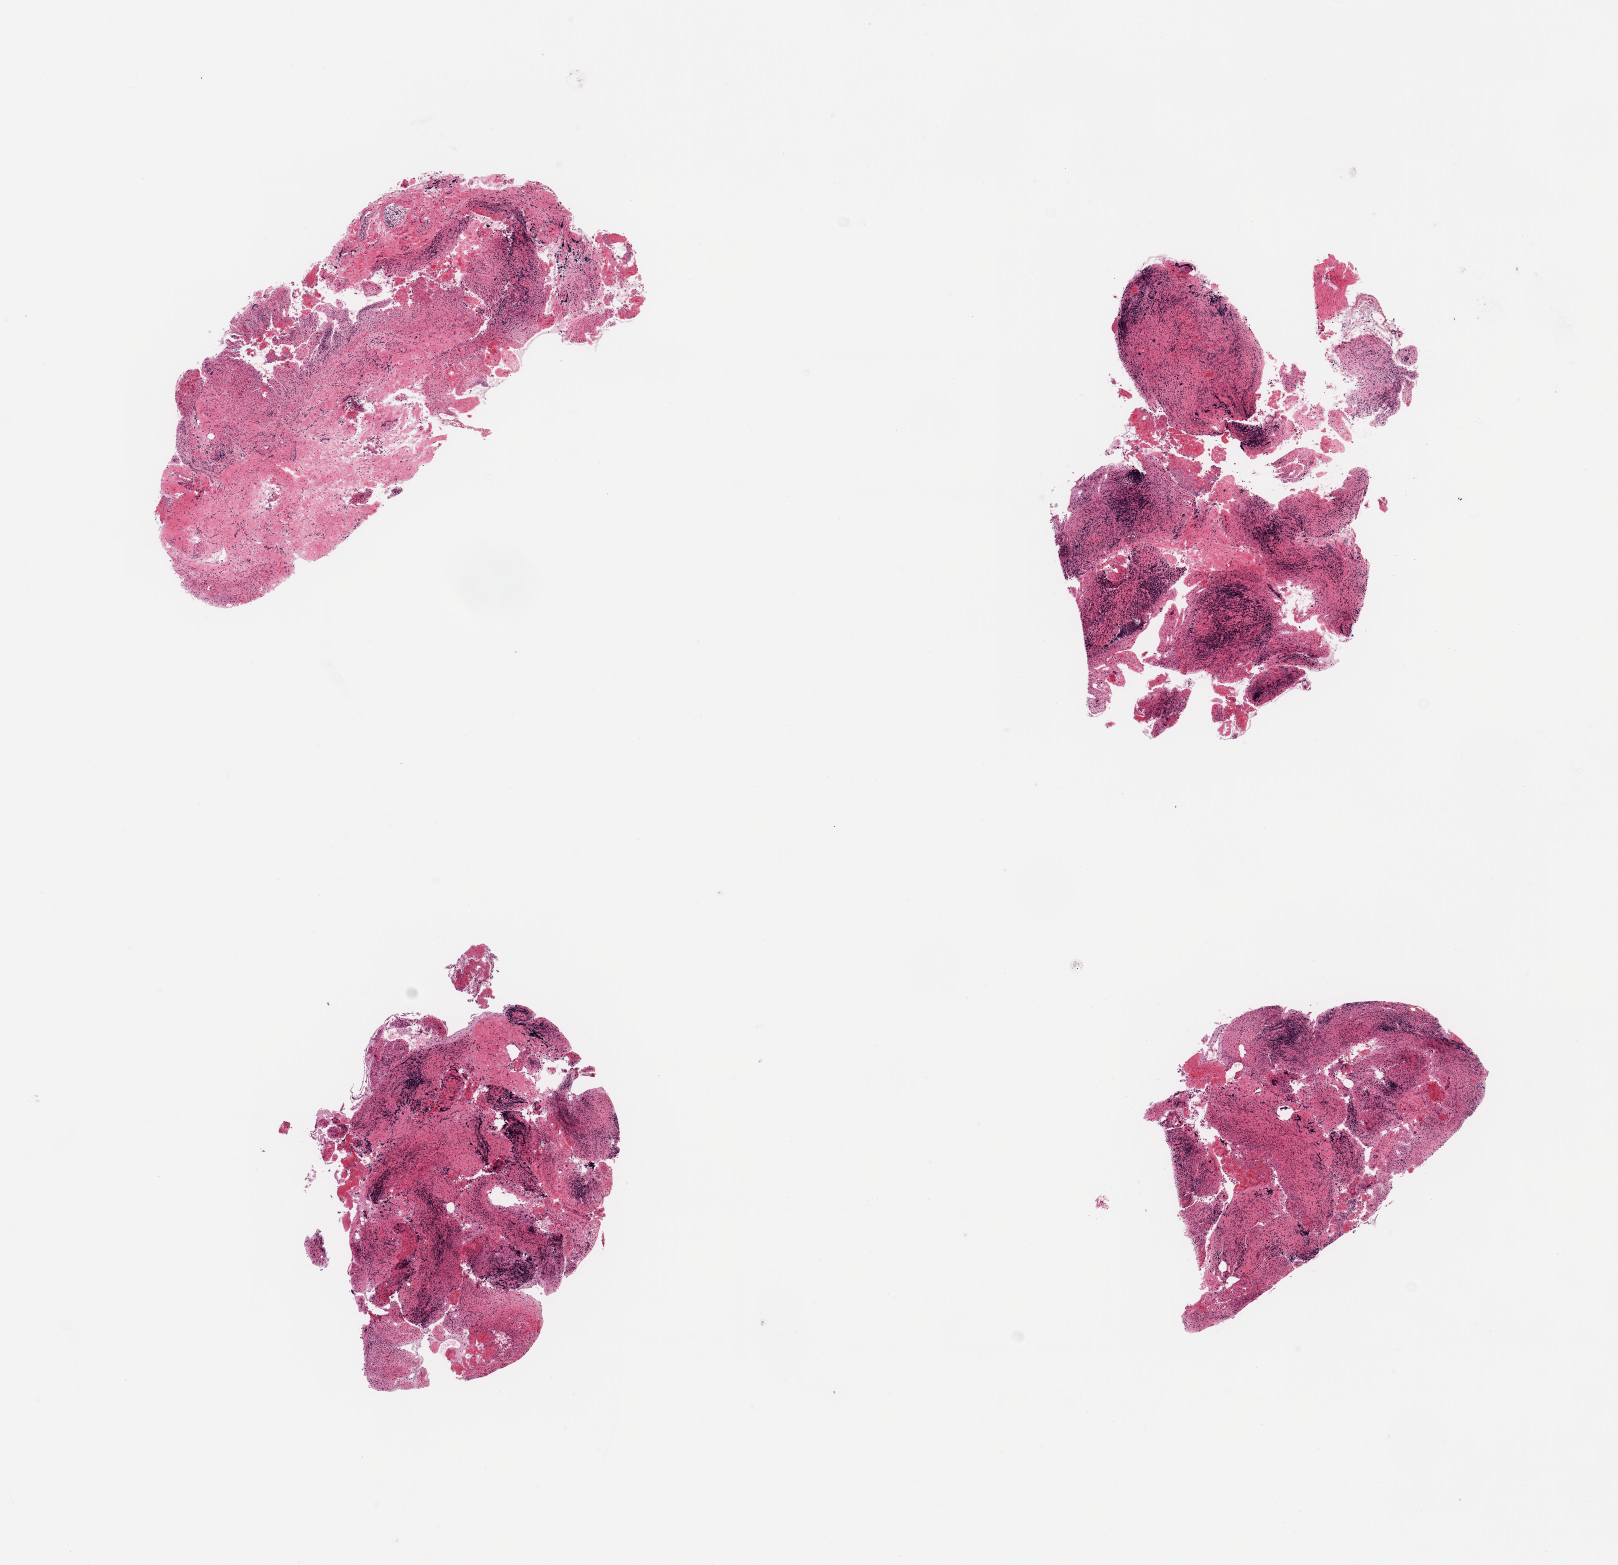
Digitized haematoxylin and eosin-stained section, brightfield, whole scanned area (about 12.8 x 12.4 mm) shown as a low-resolution overview. PAXgene-fixed paraffin-embedded (PFPE) section. Section of ileum (target tissue). Tissue donor sample. Female donor.
• pathologist's review note for this sample: 4 pieces; lymphoid tissue autolyzed